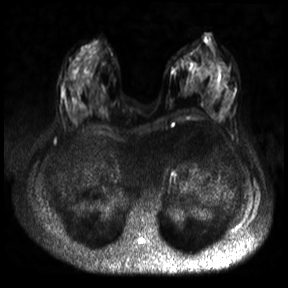
Breast MRI, one axial slice; diffusion-weighted series; image 2 of 4 stored at this slice position (different b-values; order by instance number); 3 T; 288 × 288 image matrix. Female patient.
Outlined on this slice (expert manual segmentation):
- tumour on diffusion-weighted imaging: bounding box <65,79,70,86> (left, top, right, bottom; pixels)